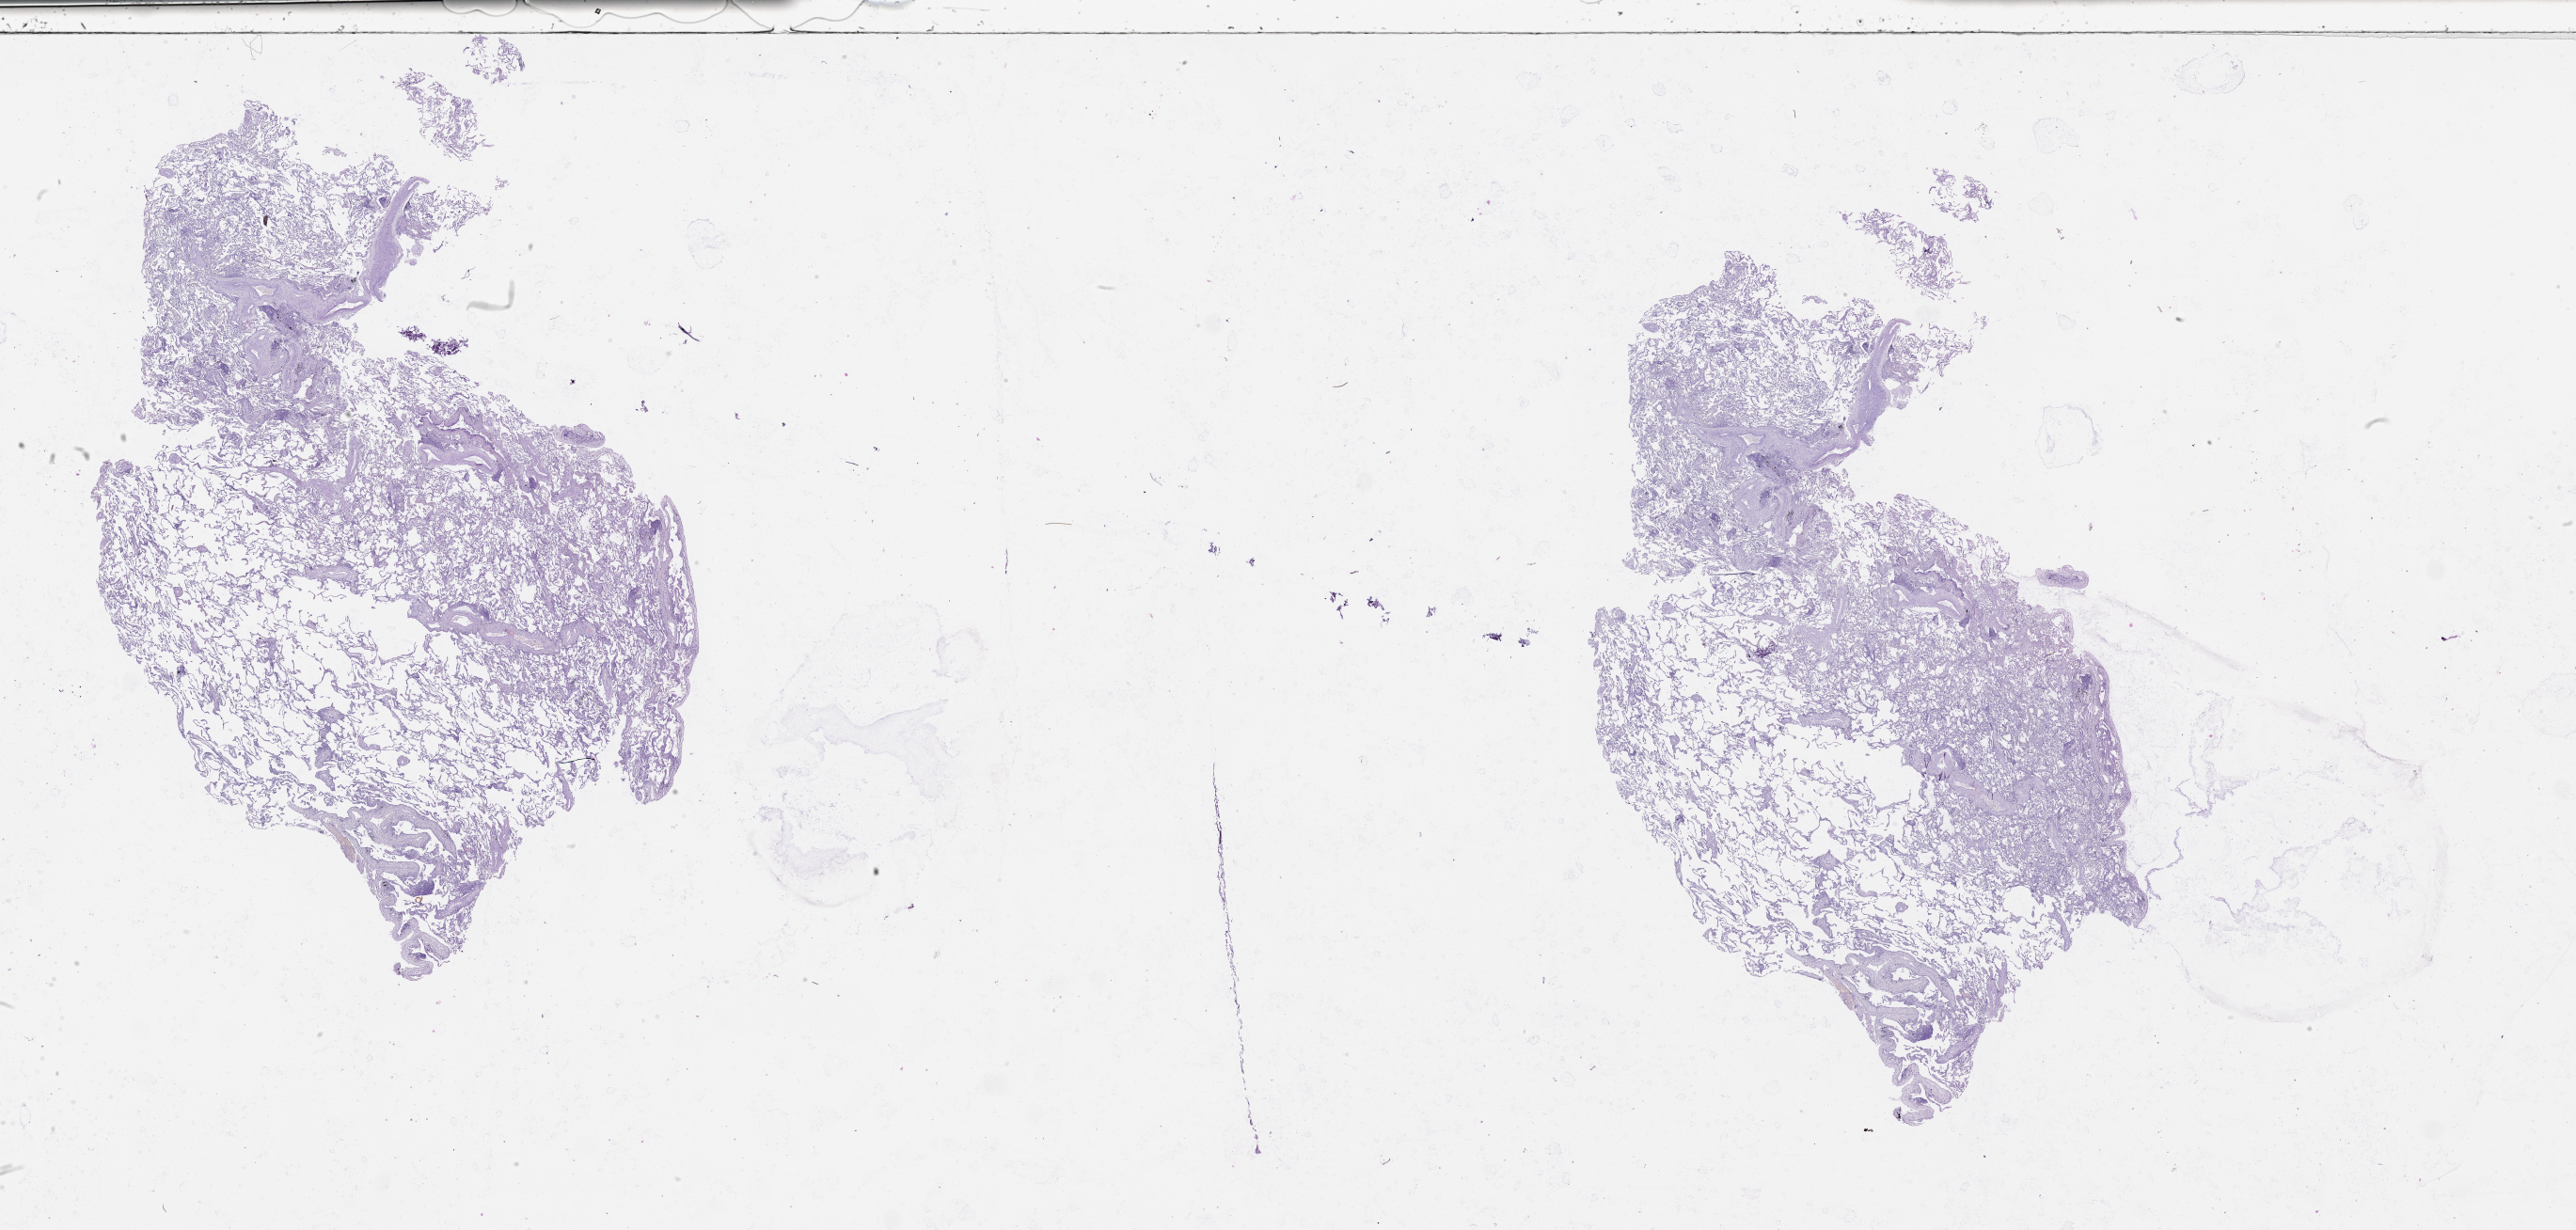
H&E whole-slide image, whole scanned area (about 44.1 x 21.1 mm, from a 20x scan) shown as a low-resolution overview; normal (non-tumour) tissue sample, lung. 68-year-old male patient.
* this section: normal (non-tumour) tissue from the same patient
* patient diagnosis (cohort enrolment): squamous cell carcinoma (lung)